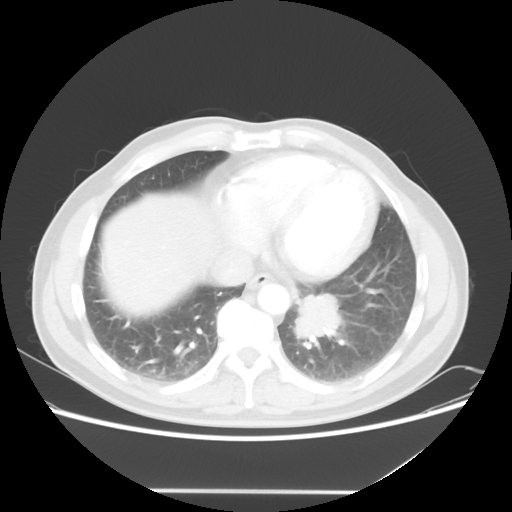
Chest CT, one axial slice. Position 19 of 56 along the scan axis. Lung window (W 1500 / L -600 HU). 5 mm slice thickness. 512 × 512 image matrix, field of view 385 × 385 mm. Patient: male, 61 years. From the clinical record (not read from this slice): clinical TNM (as recorded): T1c N0 M0.
Outlined on this slice (rectangle marked by the reading radiologist):
- lung tumour (recorded histology: adenocarcinoma): bounding box <292,290,351,350> (left, top, right, bottom; pixels)